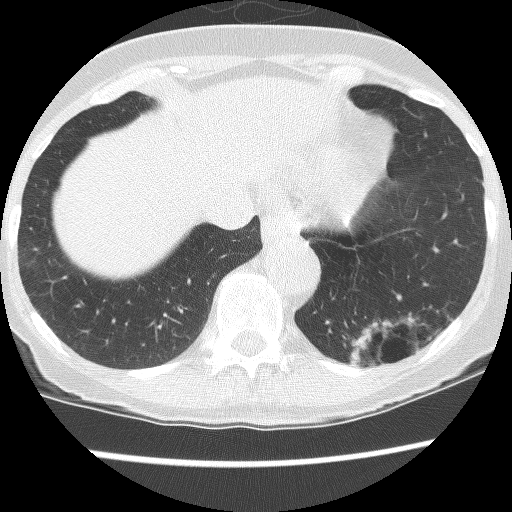
Axial slice from a low-dose chest CT screening exam. Third annual screen. Lung window (W 1500 / L -600 HU). Female, age 61 years at enrolment. Current smoker at enrolment.
Expert reader's lesion annotation, bounding box (x1, y1, x2, y2) in pixels: (335, 294, 442, 386). The screening reader recorded 2 non-calcified nodules or masses ≥4 mm on this exam; which of them this box marks is not recorded. Official screen result: positive, no significant change: stable abnormalities potentially related to lung cancer, unchanged since the prior screening exam. Later outcome: lung cancer diagnosed 166 days after this screen — non-small cell carcinoma, left lower lobe, poorly differentiated (G3), stage IB (AJCC 6th edition), 100 mm at pathology.